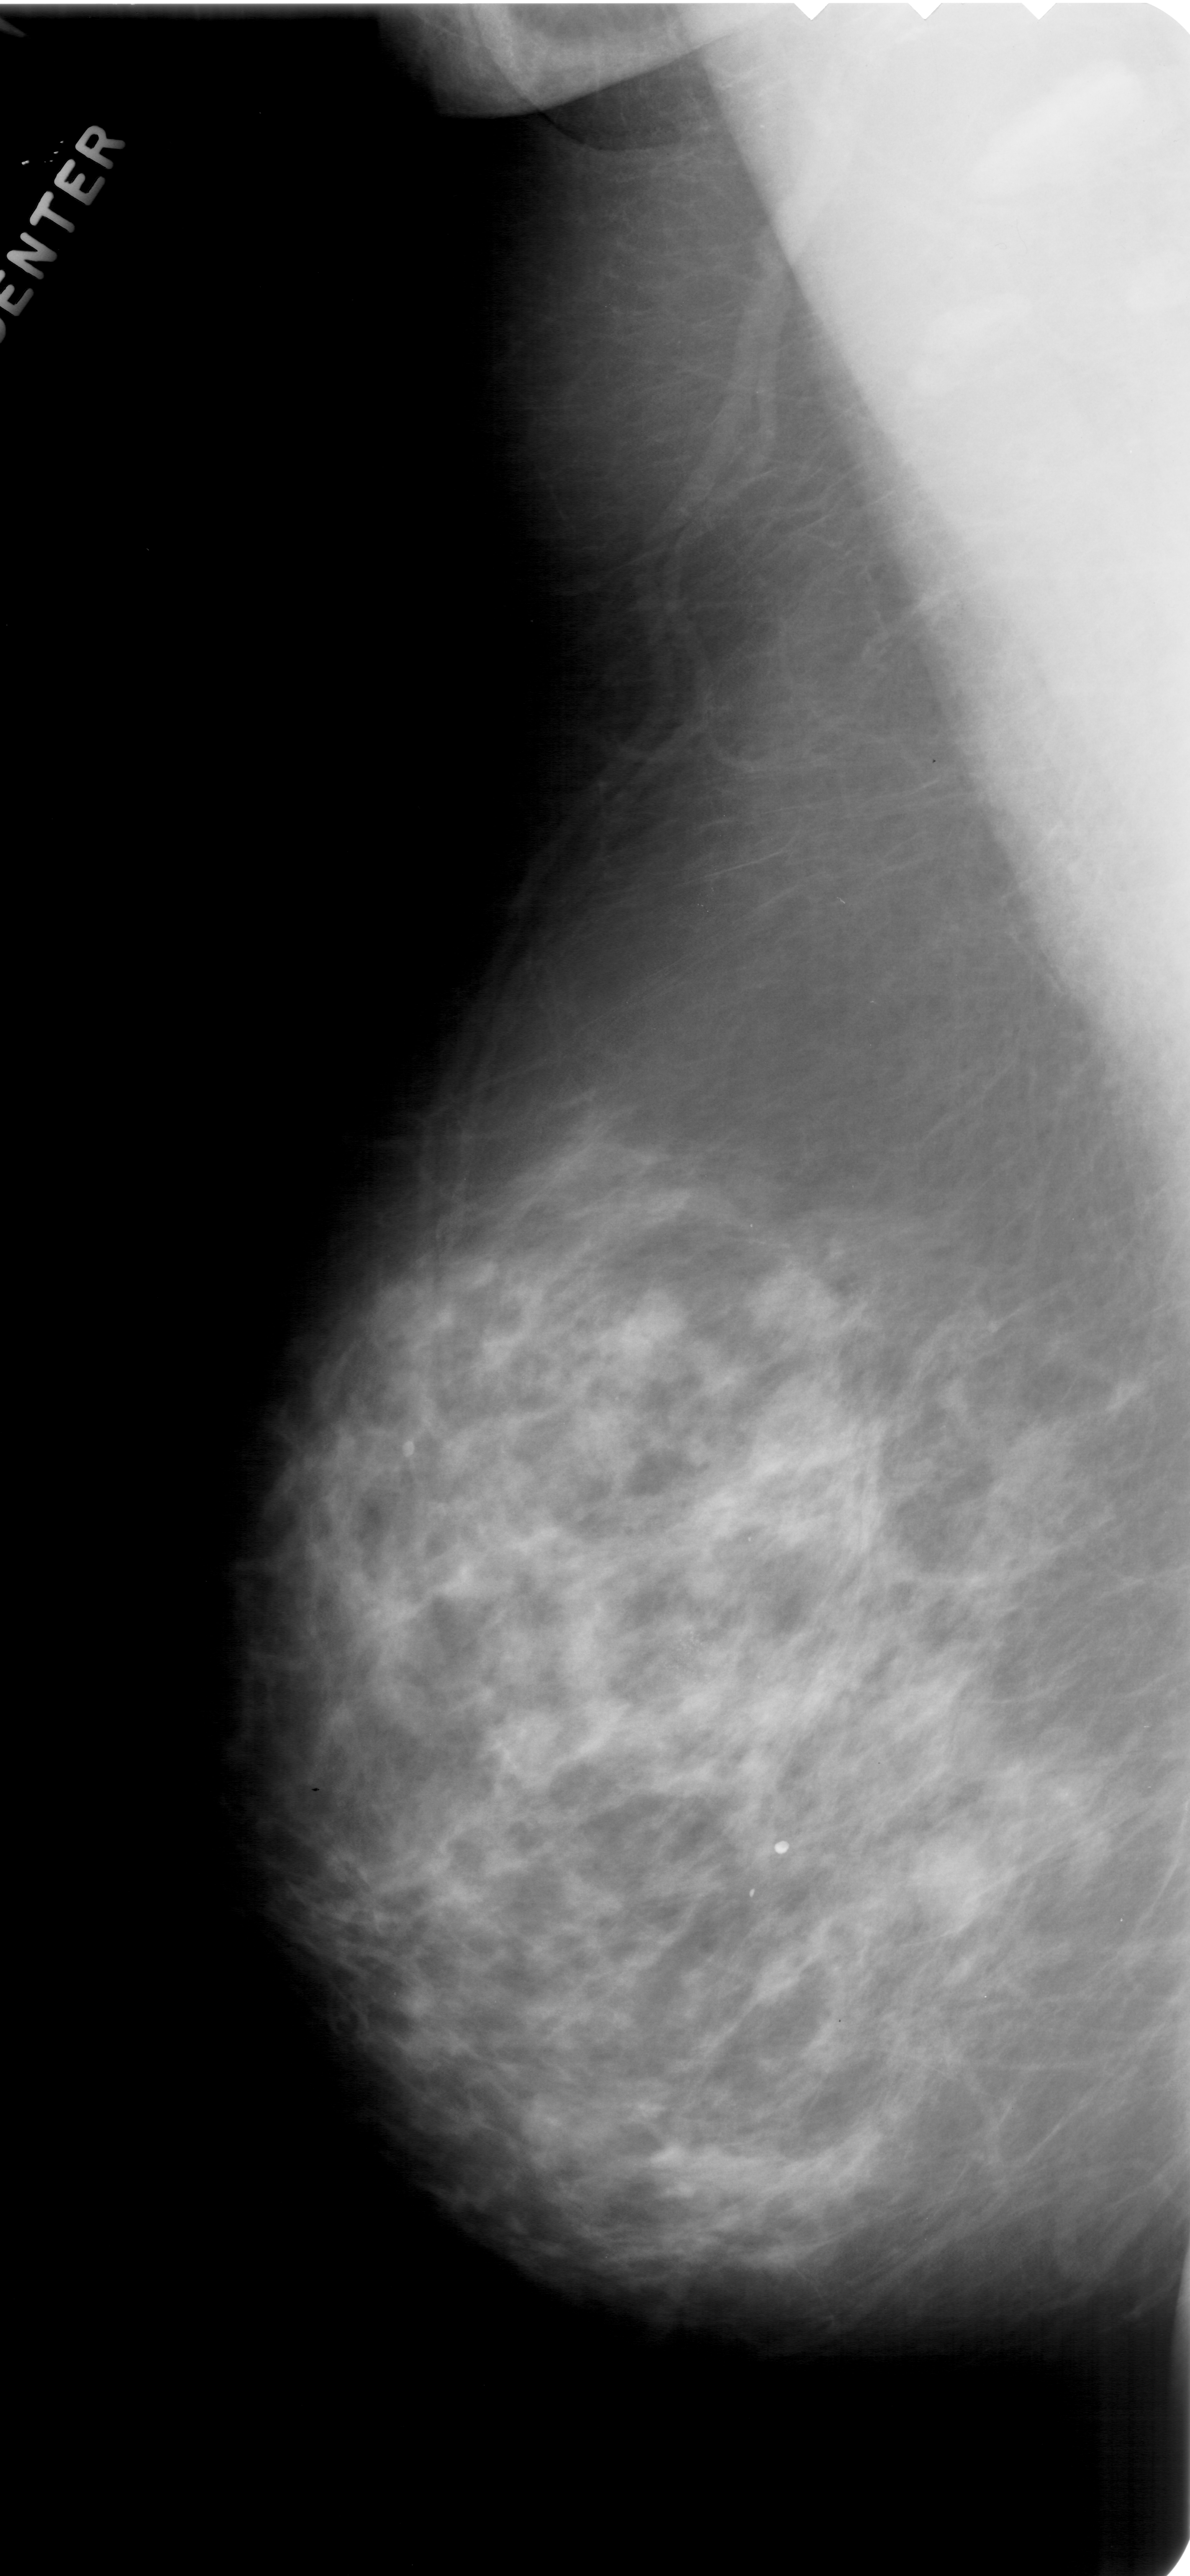
Scanned film-screen mammogram; left breast; mediolateral oblique (MLO) view; BI-RADS breast density category 3 (scale 1–4); 1190 × 2576 image matrix.
Expert-marked regions of interest on this image (one box per marked abnormality):
- calcifications, morphology pleomorphic, distribution clustered; BI-RADS assessment category 4; pathology result (as recorded, not read from the image): malignant: bounding box <663,1617,728,1701> (left, top, right, bottom; pixels)